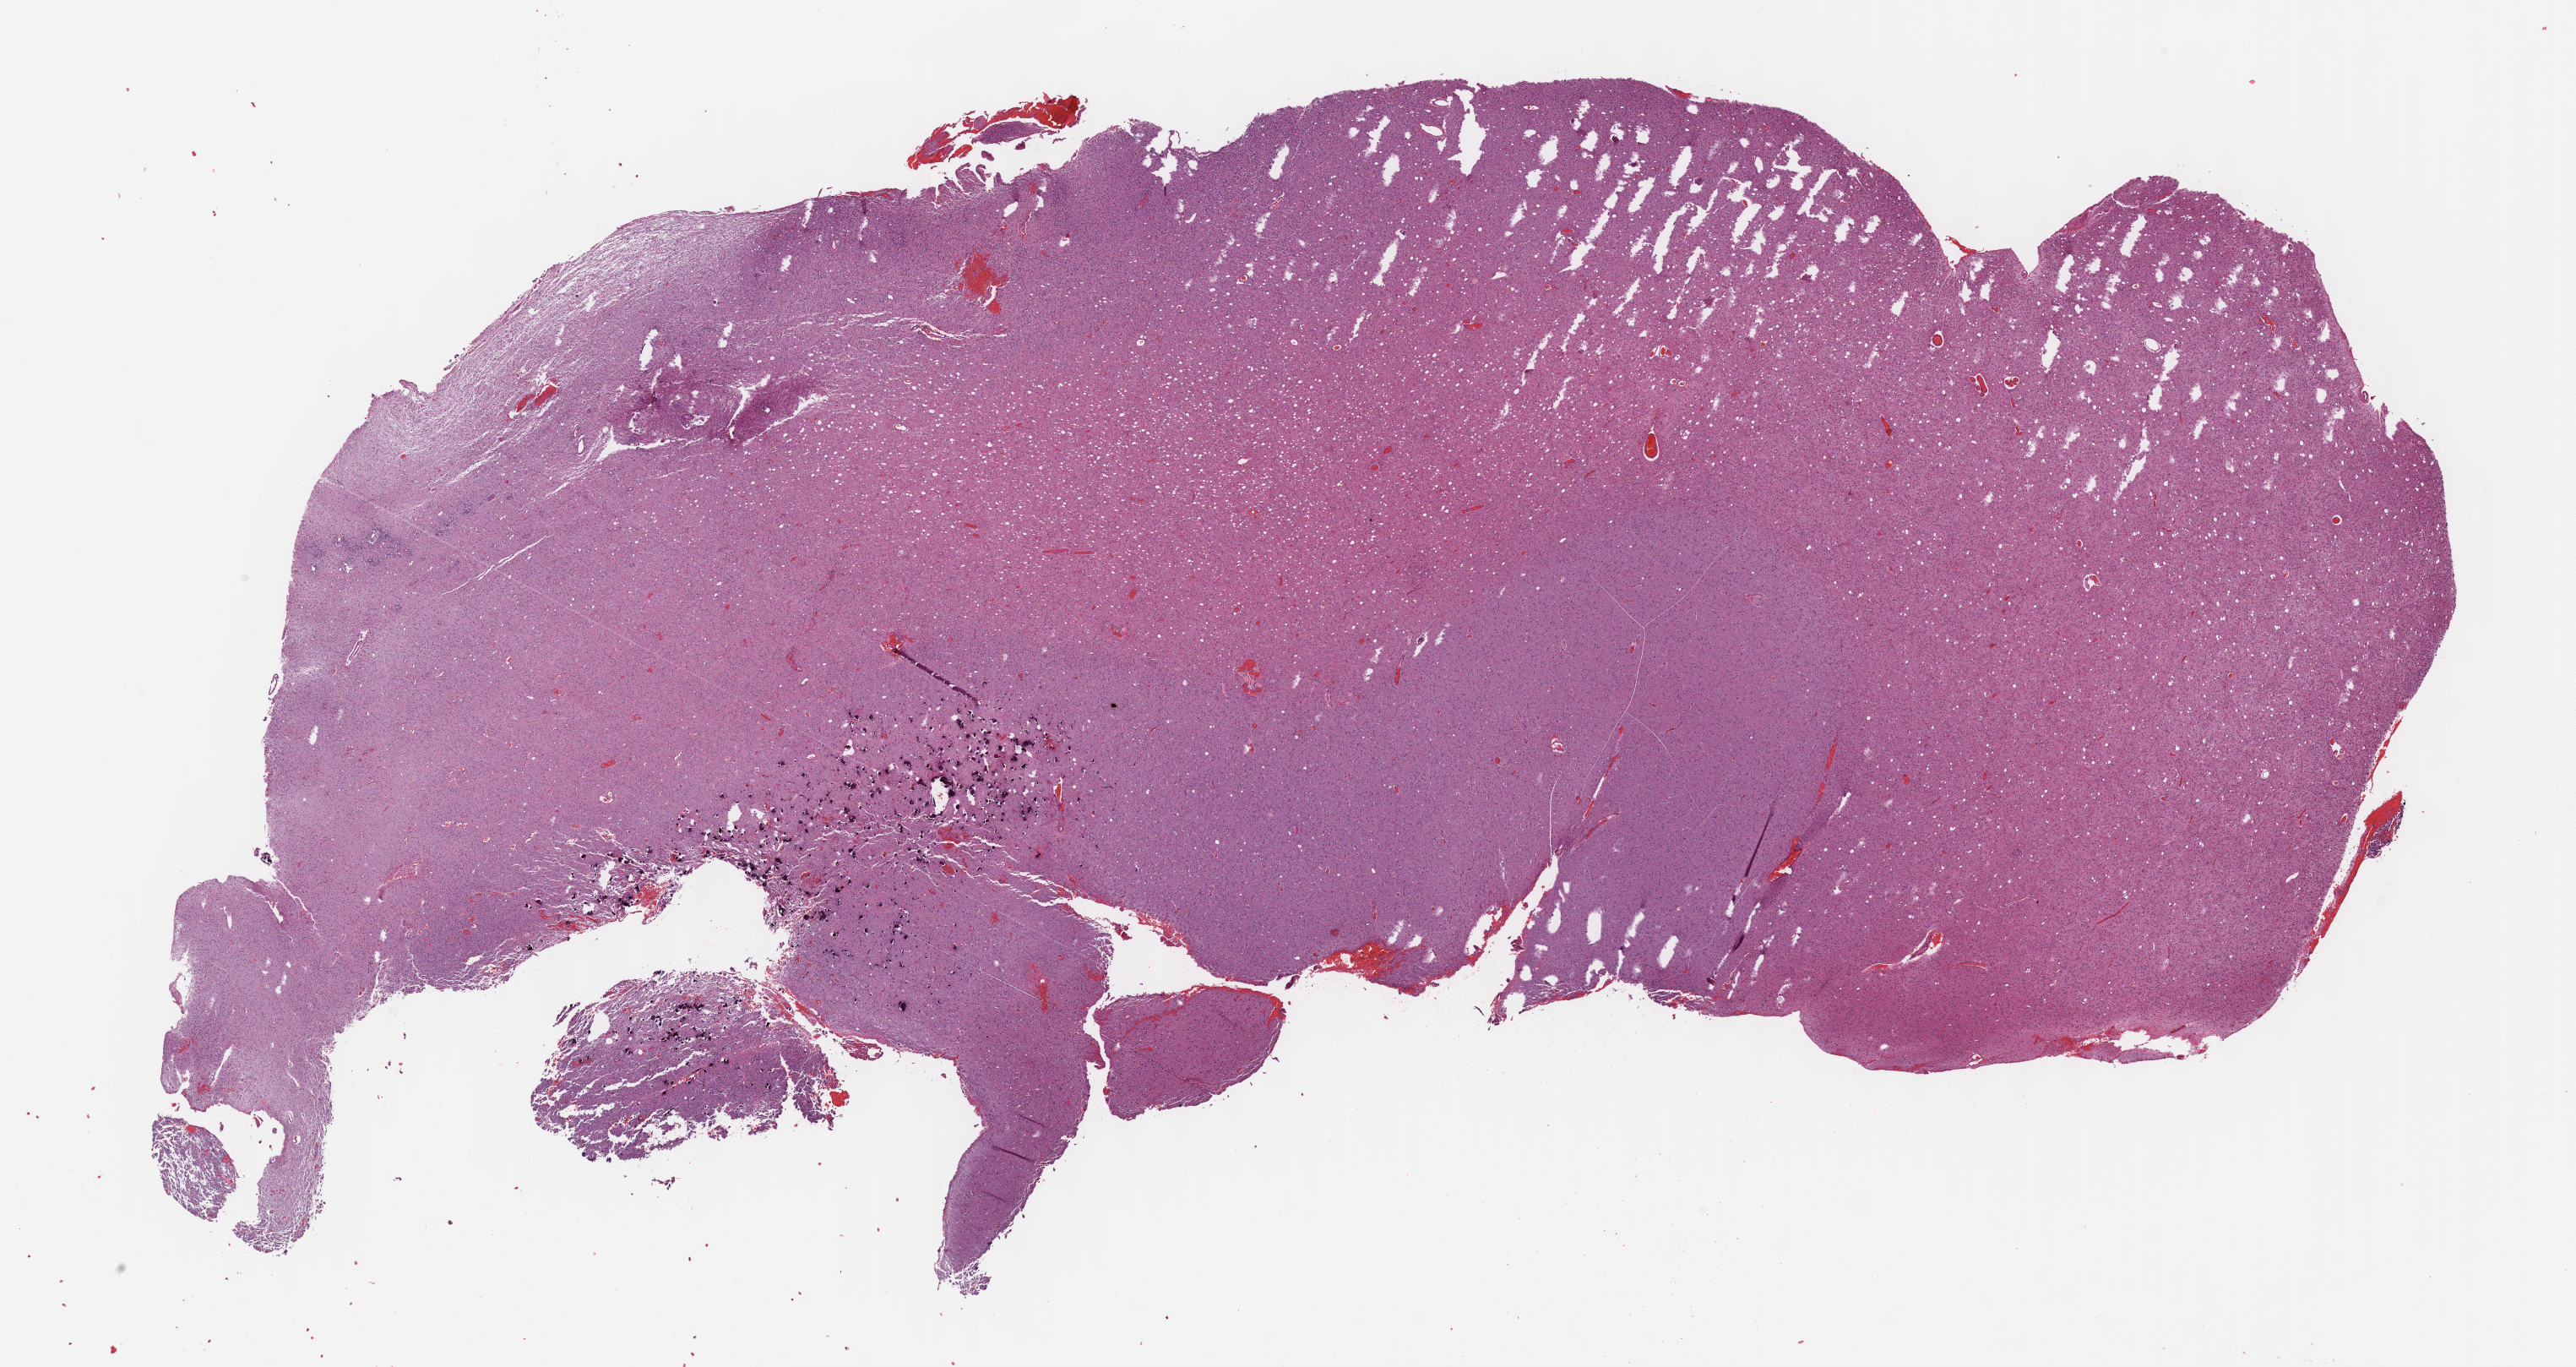
Hematoxylin and eosin (H&E) stained whole-slide image, a low-resolution overview of the entire scanned area, about 24.7 x 13.1 mm, formalin-fixed paraffin-embedded (FFPE) diagnostic section, brain, primary tumour sample. Patient: male, age at initial diagnosis 58 years. Histologic grade: G3 (poorly differentiated).
Histologic diagnosis: Mixed glioma (cerebrum).